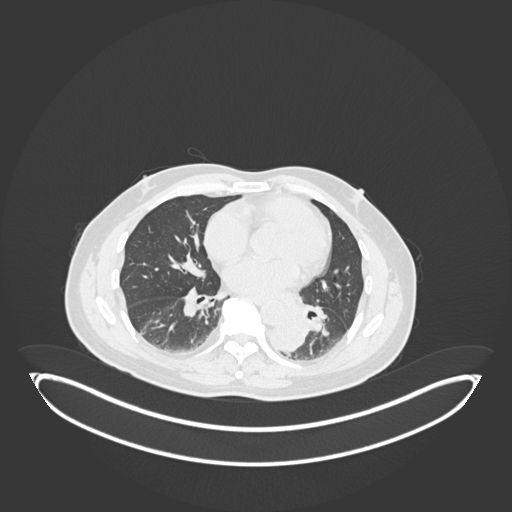
Chest CT, one axial slice. Reconstruction kernel B30f. 120 kVp. Lung window (W 1500 / L -600 HU). 1 mm slice thickness. 512 × 512 image matrix, field of view 500 × 500 mm. Patient: male, 54 years. From the clinical record (not read from this slice): clinical TNM (as recorded): T3 N0 M0.
Outlined on this slice (rectangle marked by the reading radiologist):
- lung tumour (recorded histology: squamous cell carcinoma): box from (x=267, y=307) to (x=311, y=355) px